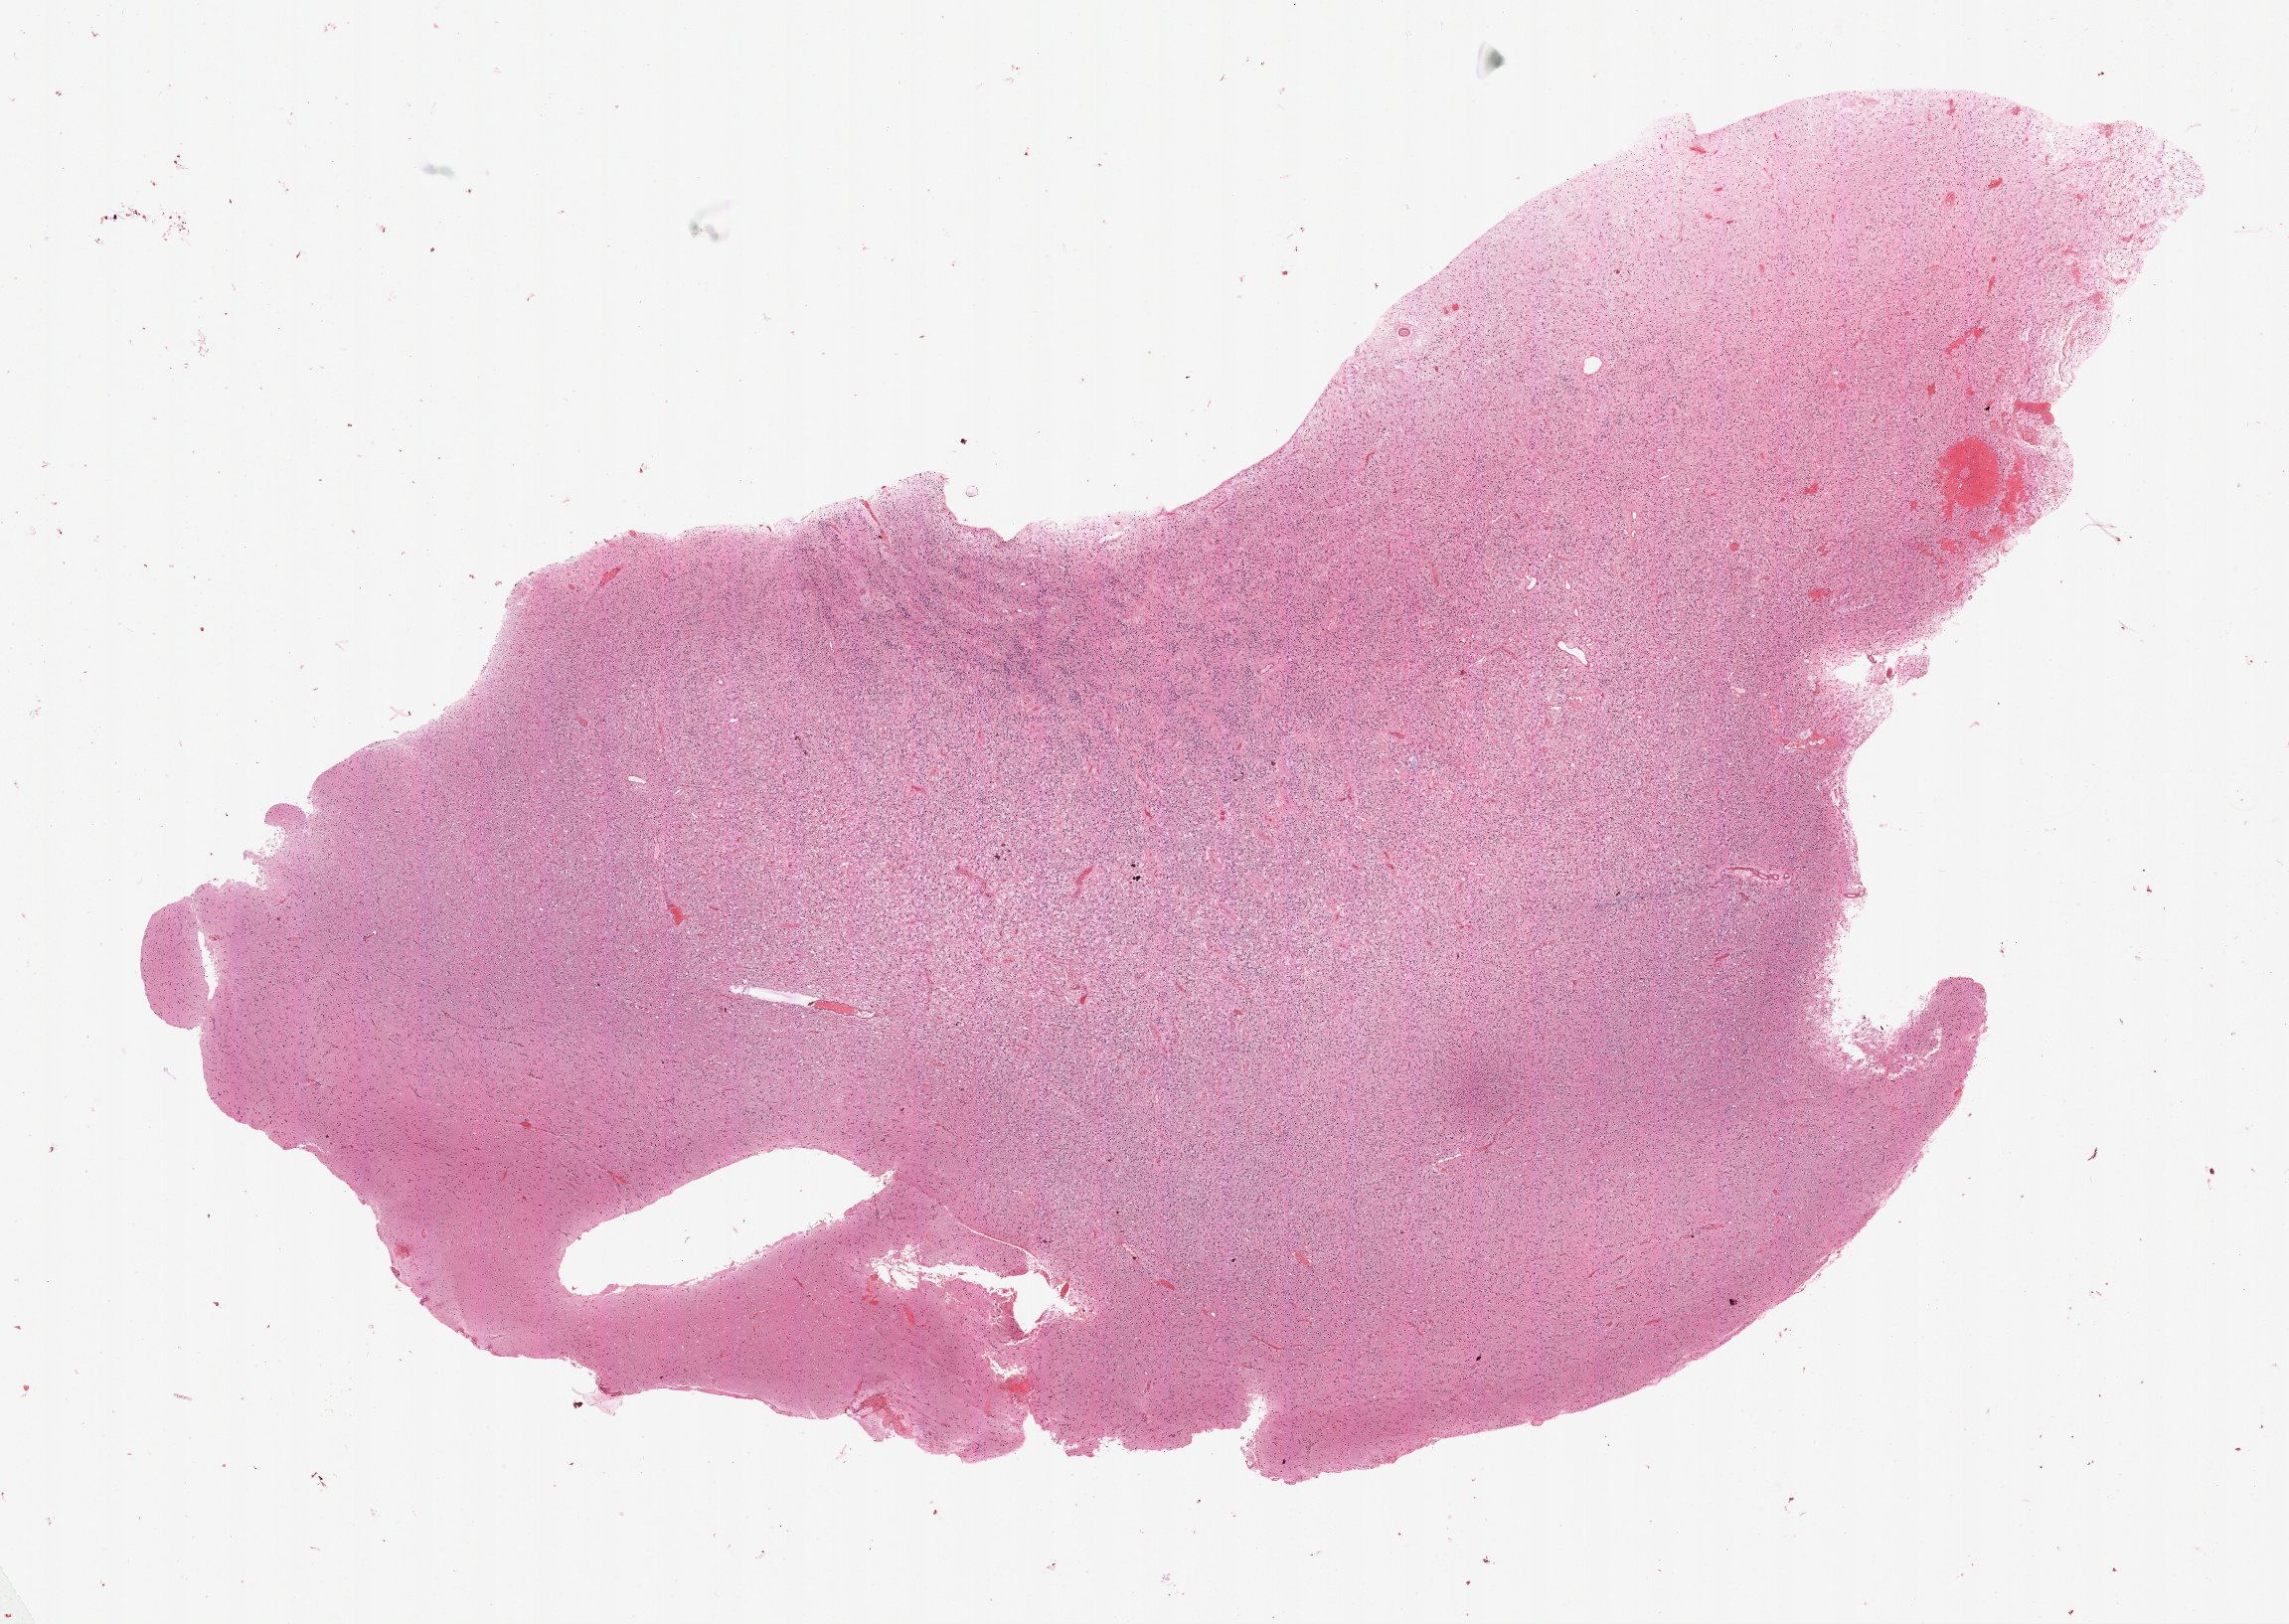
Digitized H&E tissue section (whole slide), low-resolution overview of the scanned area, about 18.6 x 13.2 mm (slide scanned at 40x). Formalin-fixed paraffin-embedded (FFPE) diagnostic section. Brain, primary tumour sample. Patient: female, age at initial diagnosis 44 years. Histologic grade: G3 (poorly differentiated).
• pathologic diagnosis: Mixed glioma (cerebrum)
• laterality: right